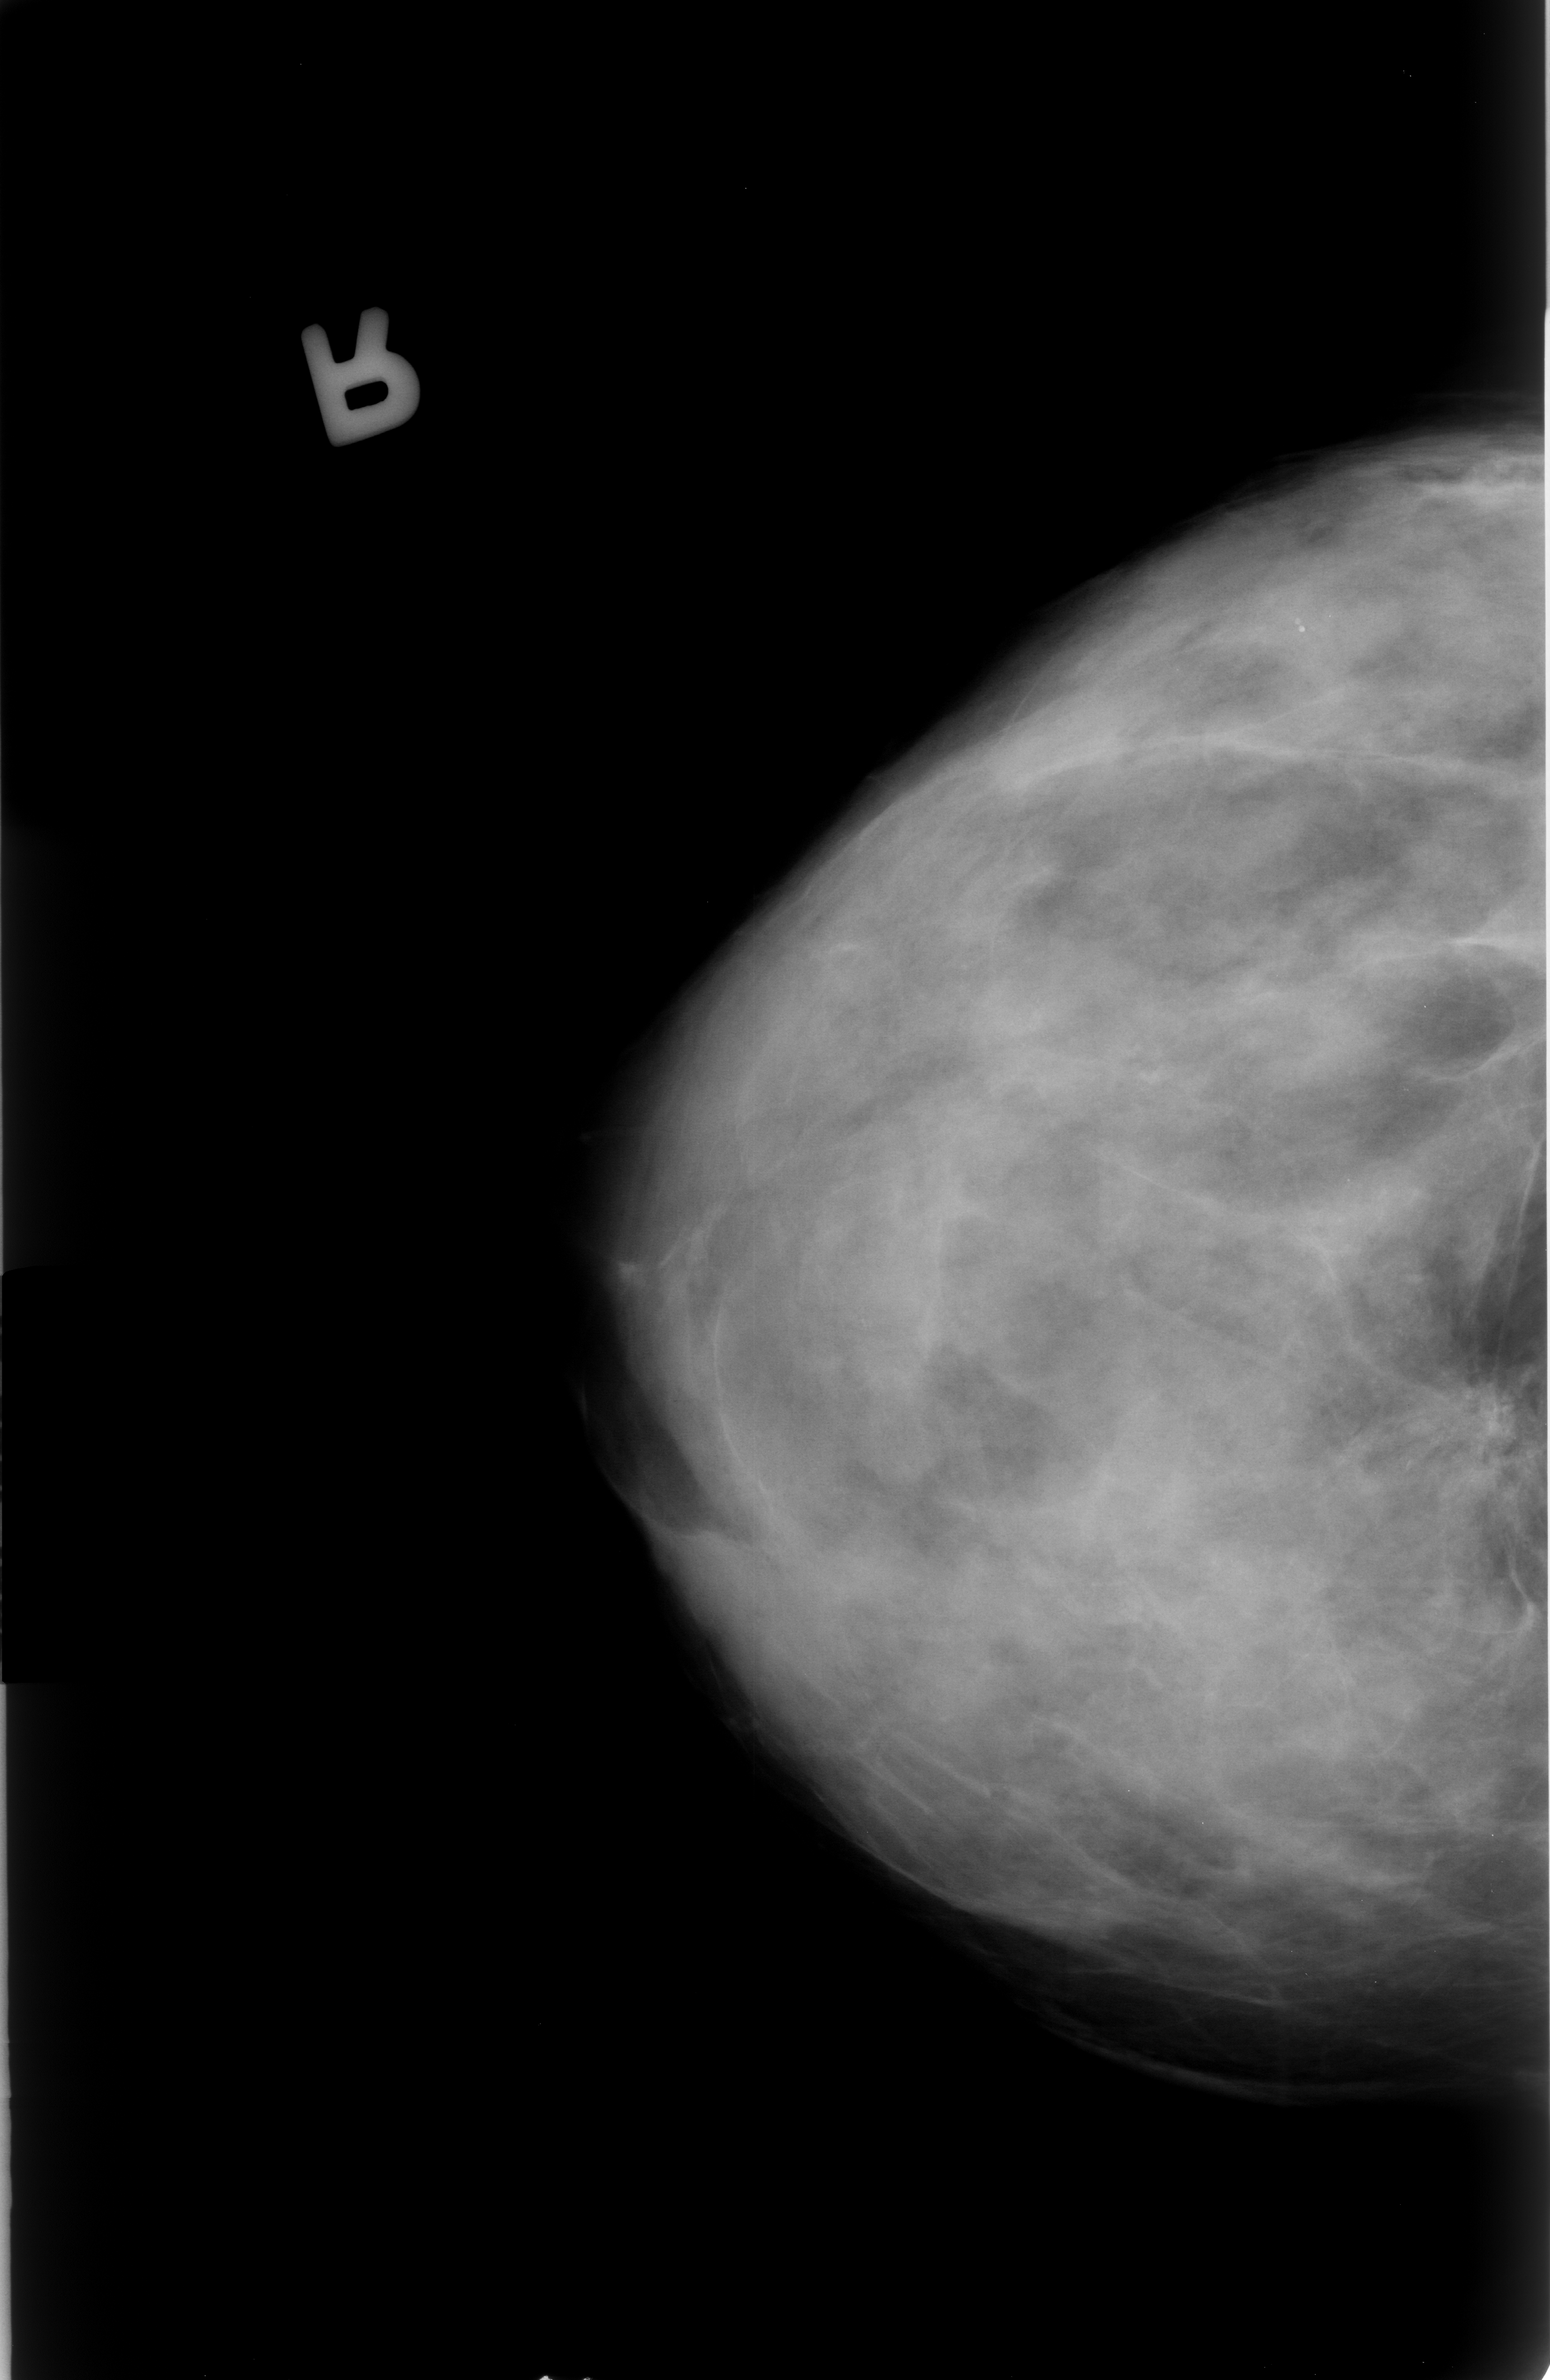
Mammogram (digitized film); right breast; CC view; BI-RADS breast density category 4 (scale 1–4).
- Marked abnormality: calcifications, morphology punctate / pleomorphic, distribution clustered; BI-RADS assessment category 4; subtlety rating 3 on a 1 (subtle) to 5 (obvious) scale; pathology (as recorded): malignant.